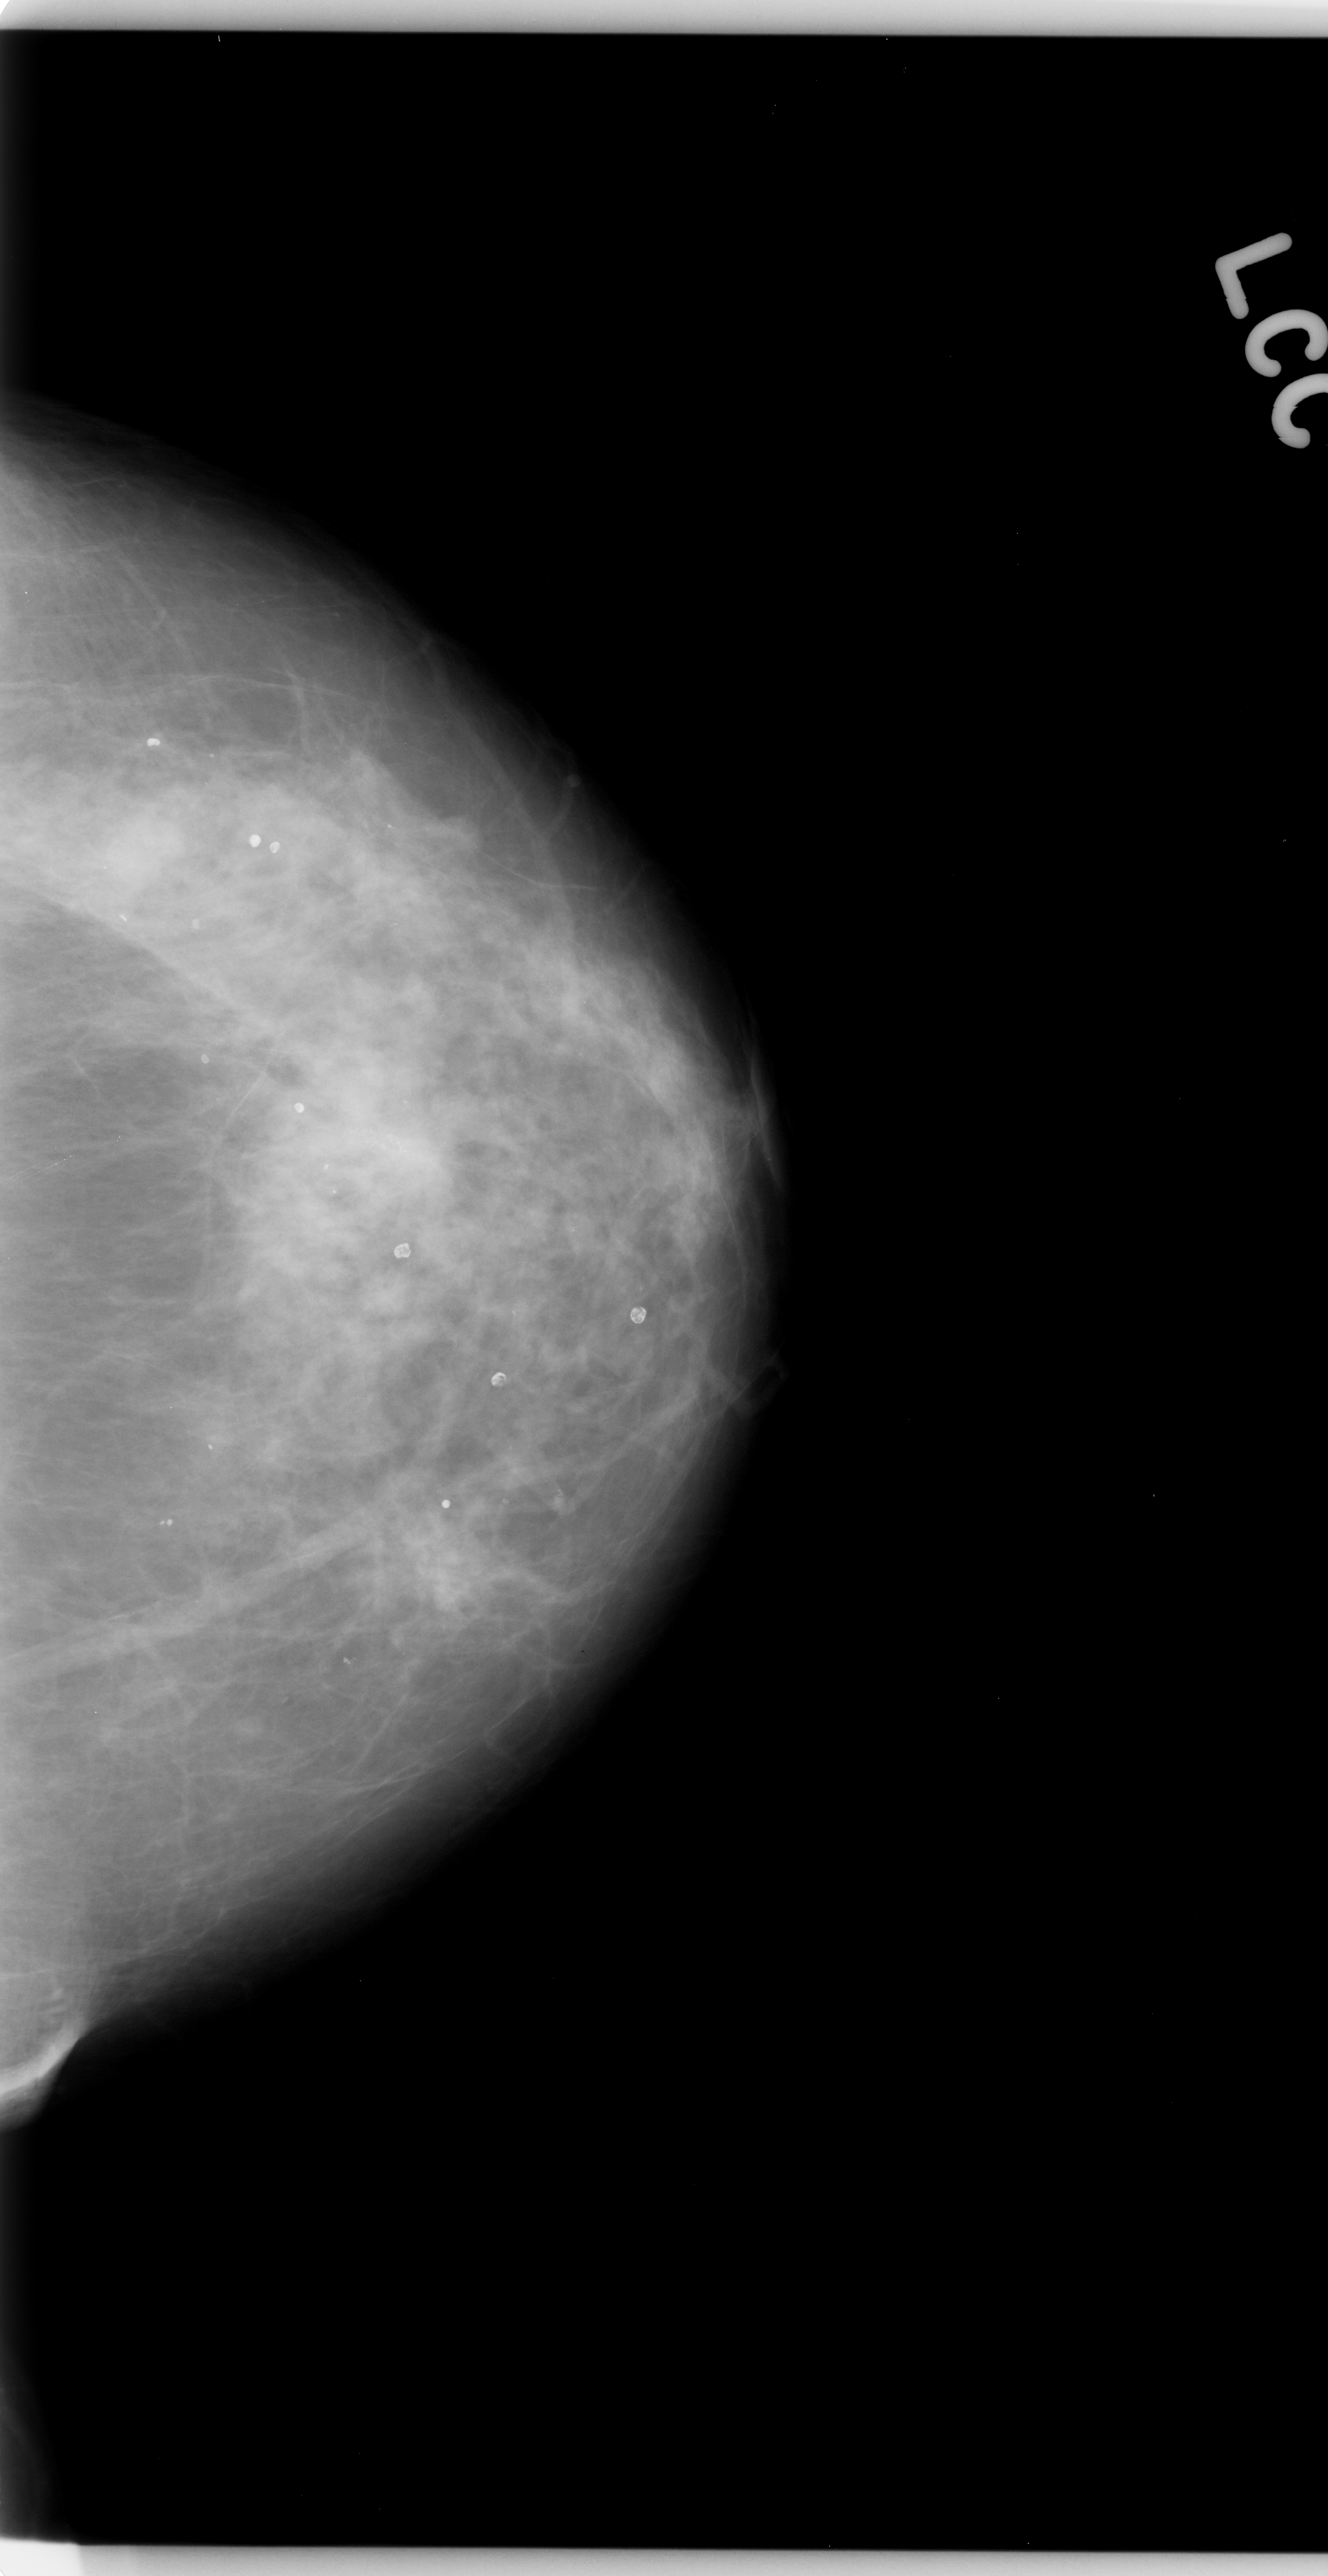
Mammogram (digitized film). Left breast. CC view. 1328 × 2576 image matrix.
Expert-marked regions of interest on this image (one box per marked abnormality):
- calcifications, morphology amorphous, distribution clustered; BI-RADS assessment category 5; pathology result (as recorded, not read from the image): malignant: bounding box [x1, y1, x2, y2] px = [310, 1059, 478, 1228]